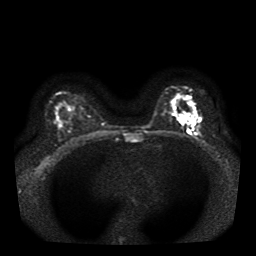
Breast MRI, one axial slice; position 26 of 41 along the scan axis; diffusion-weighted series; image 2 of 4 stored at this slice position (different b-values; order by instance number); 1.5 T; 256 × 256 image matrix. Female patient.
Outlined on this slice (expert manual segmentation):
- tumour on diffusion-weighted imaging: bounding box [x1, y1, x2, y2] px = [180, 111, 195, 125]